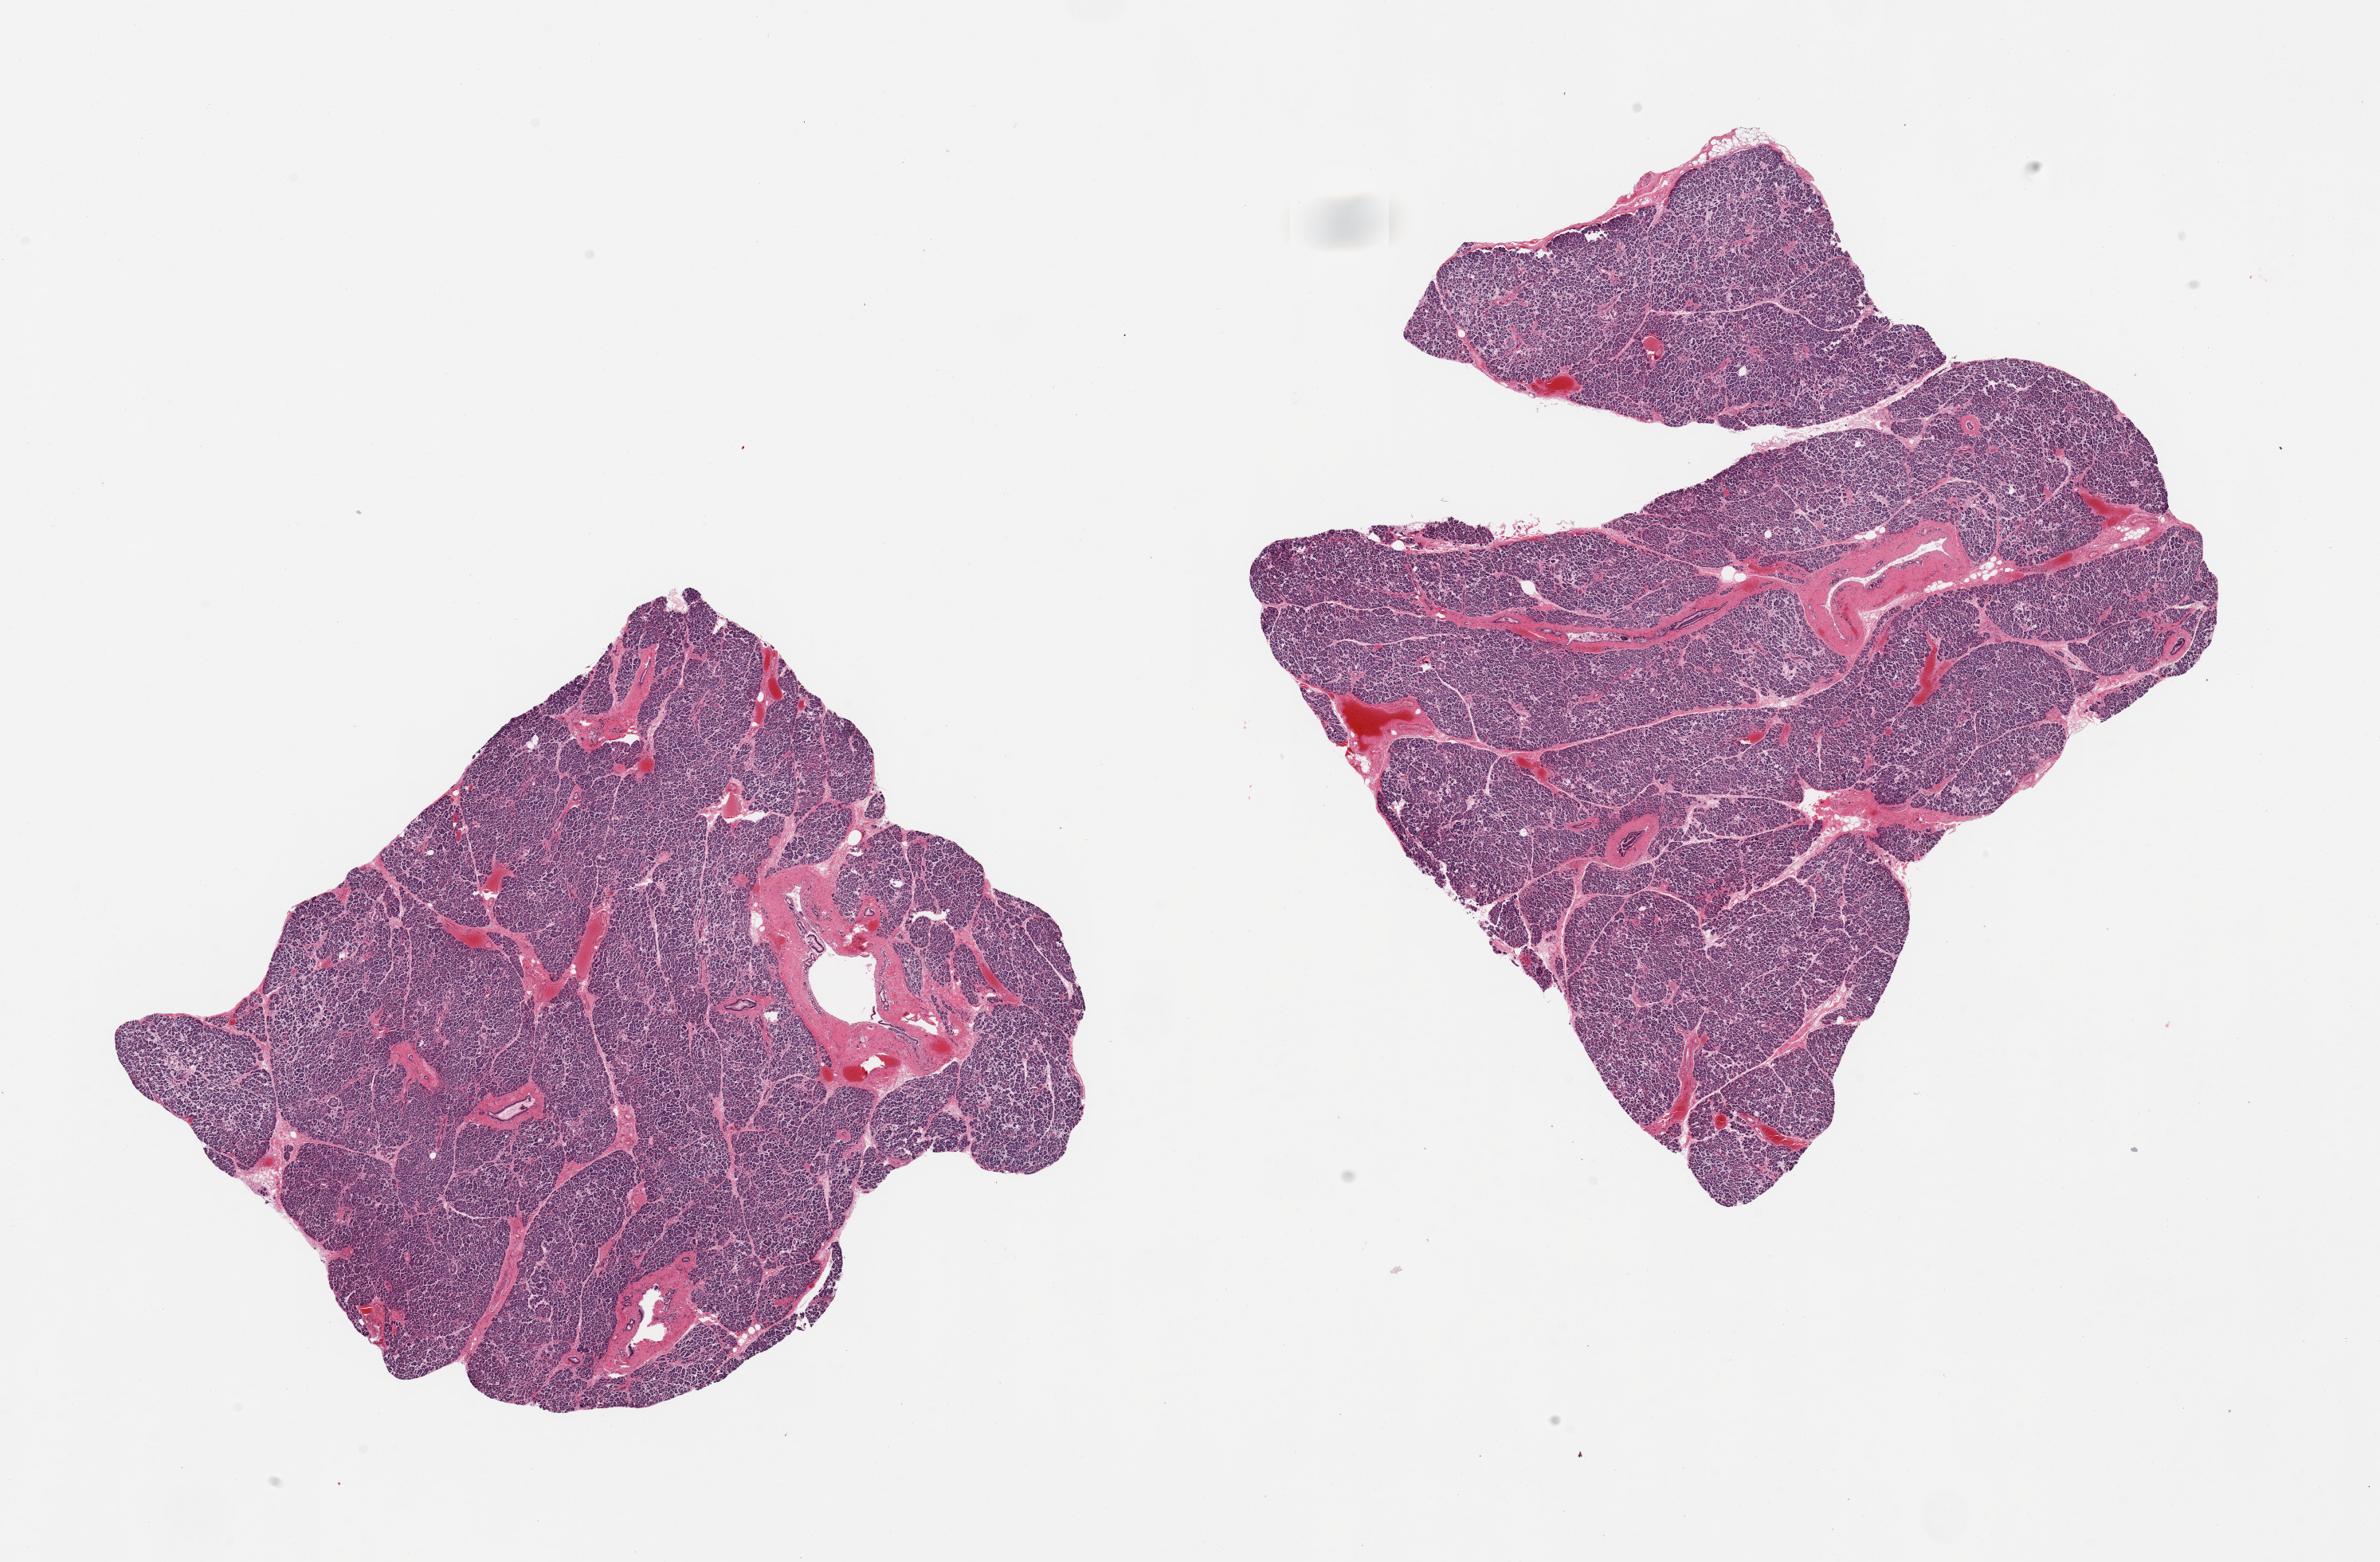
Whole-slide image, haematoxylin and eosin stain, brightfield — shown as a low-resolution overview of the whole scanned area (about 23.6 x 15.5 mm), PAXgene-fixed, paraffin-embedded tissue, section of pancreas (target tissue), tissue donor sample. Donor: female.
Review note (as recorded): 2 pieces, approaching score '2', some Islets still reasonably well-preserved.